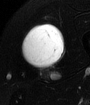
MRI of an extremity soft-tissue mass, one axial slice. T2-weighted fat-saturated. MR volume resampled by the dataset authors to the PET/CT grid (not the native acquisition matrix). 3.27 mm slice thickness. 90 × 105 image matrix, field of view 88 × 103 mm. Male patient. Case-level facts recorded for this patient, not image findings: histological type: mixoid liposarcoma; grade: low; site of the primary tumour: left thigh.
Outlined on this slice (expert contour drawn on MRI and transferred to this co-registered scan by the dataset authors):
- gross tumour volume (mass): box from (x=21, y=25) to (x=63, y=70) px